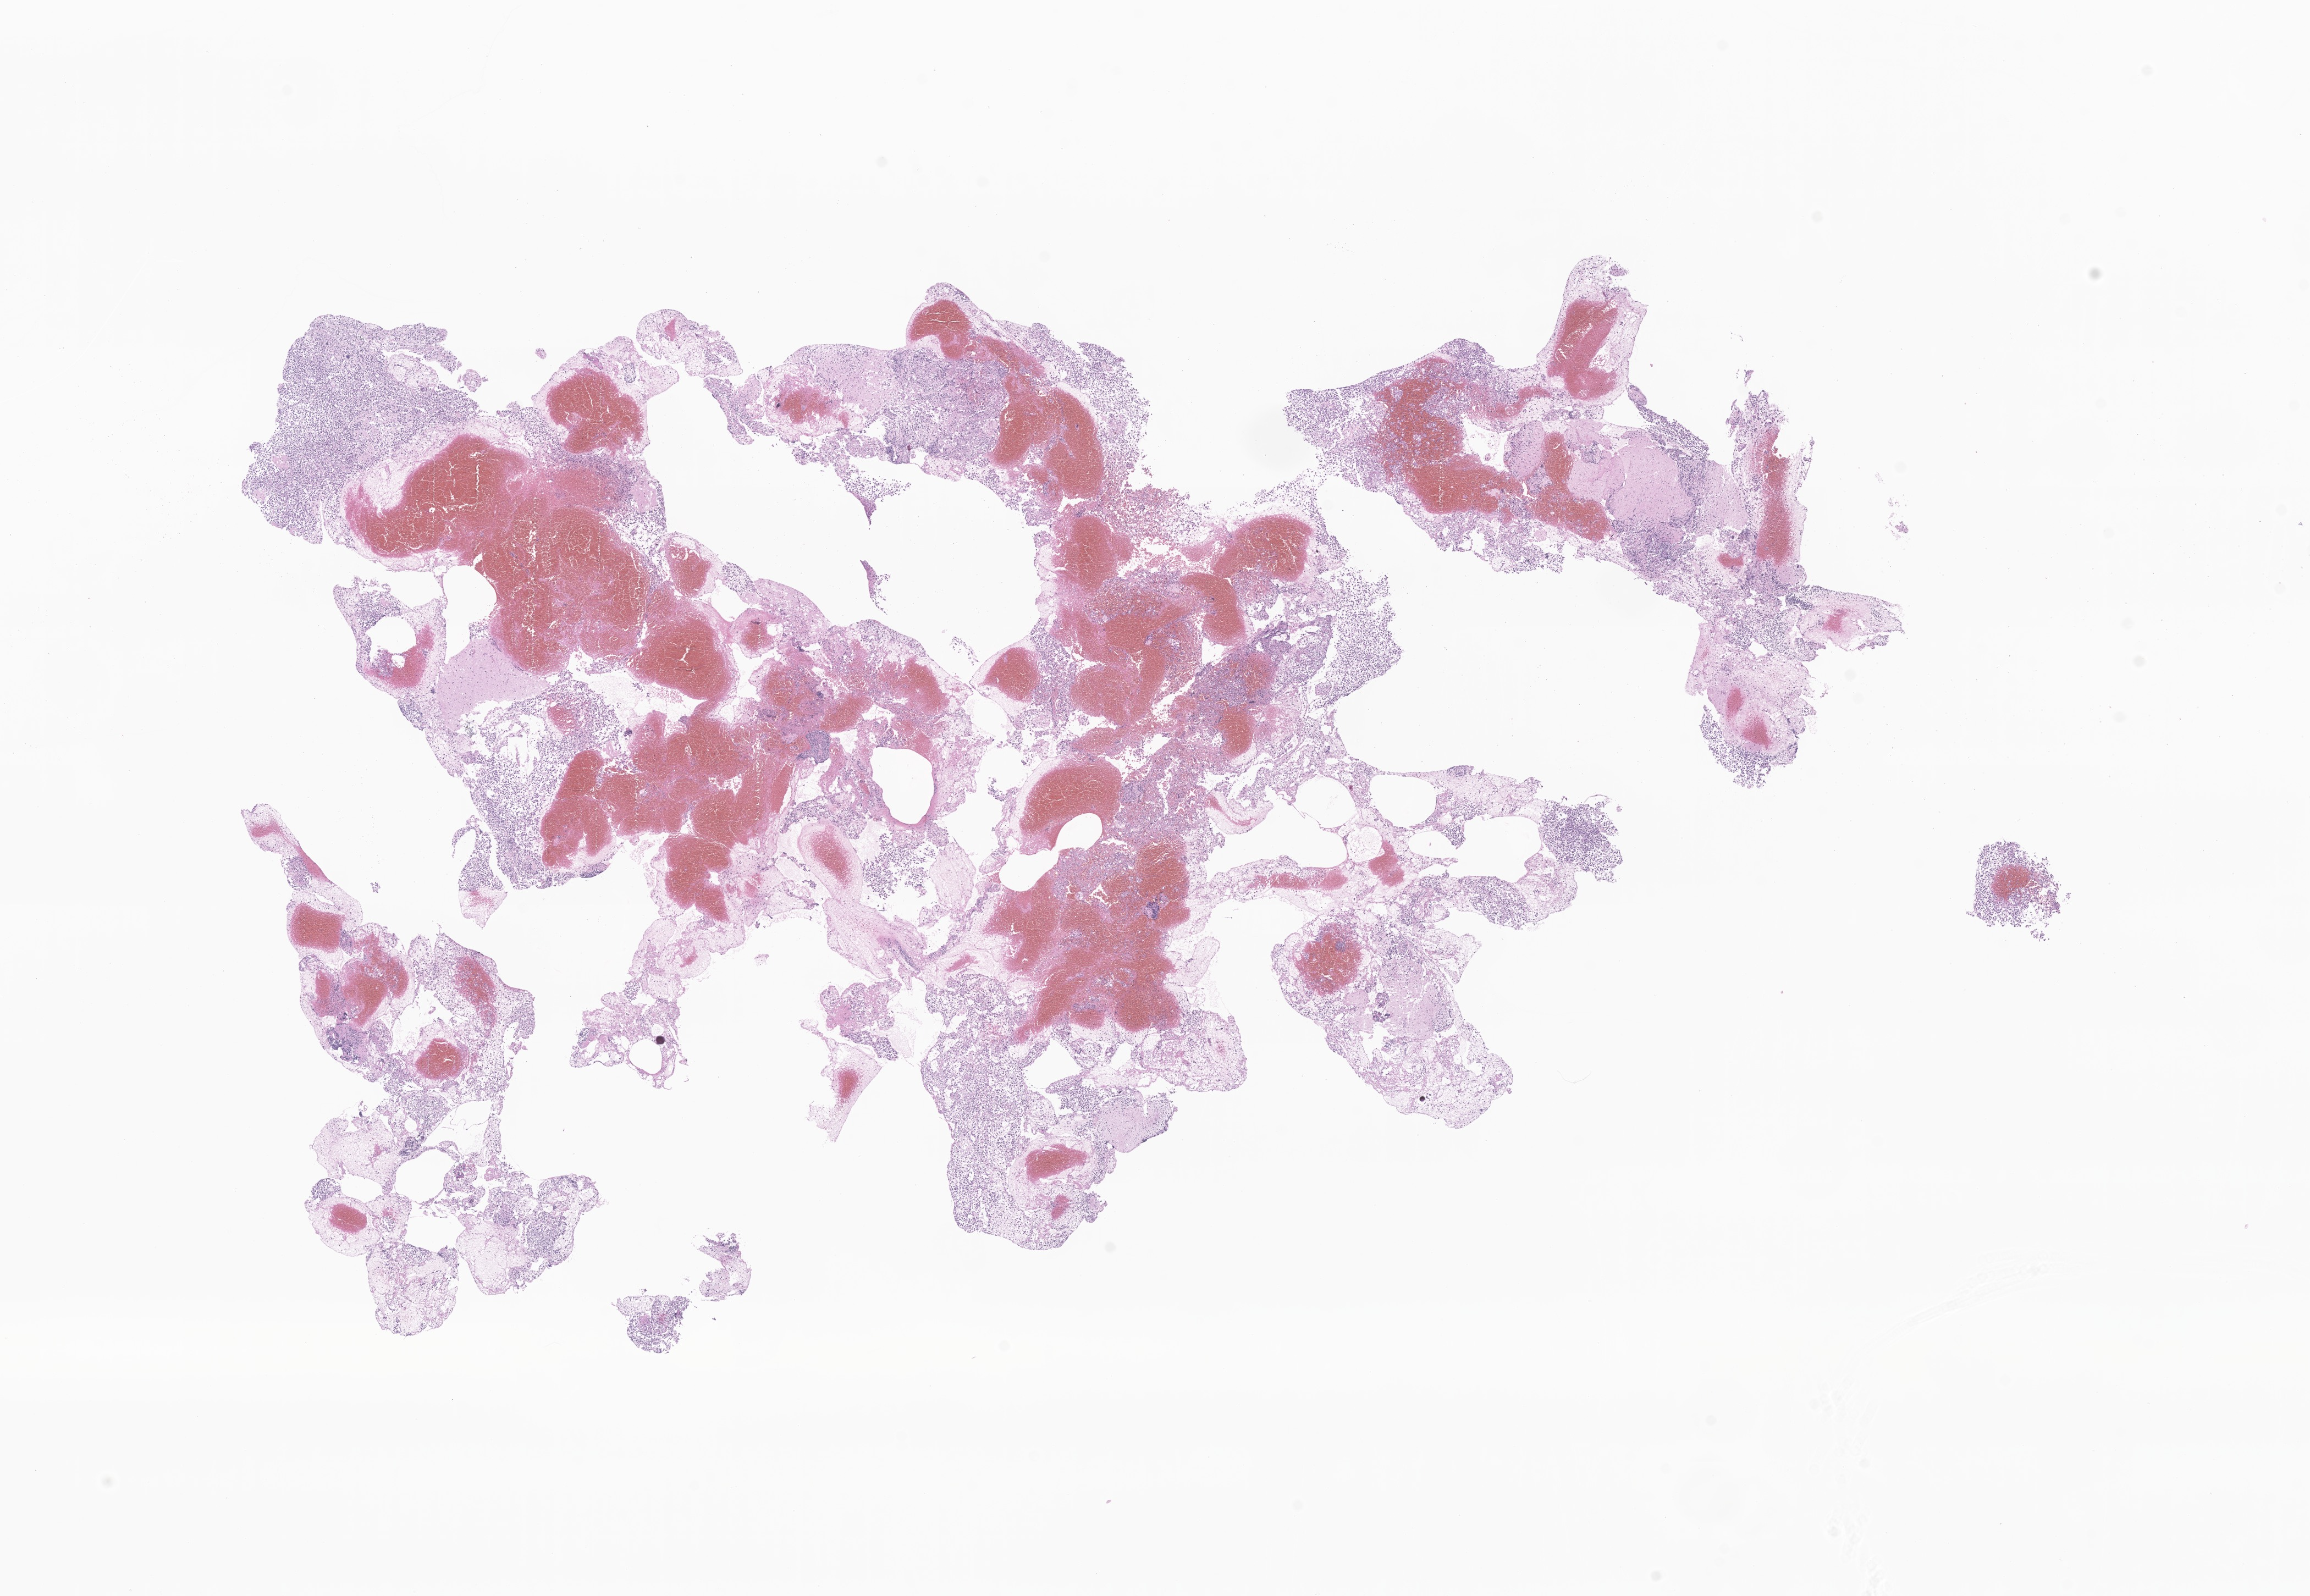
Whole-slide image, haematoxylin and eosin stain of tumor tissue from the brain stem — shown as a low-resolution overview of the whole scanned area (about 17.7 x 12.2 mm), formalin-fixed paraffin-embedded section. Male patient, age 213 months (17 years 9 months).
Diagnosis (ICD-O-3 morphology term): Germinoma.